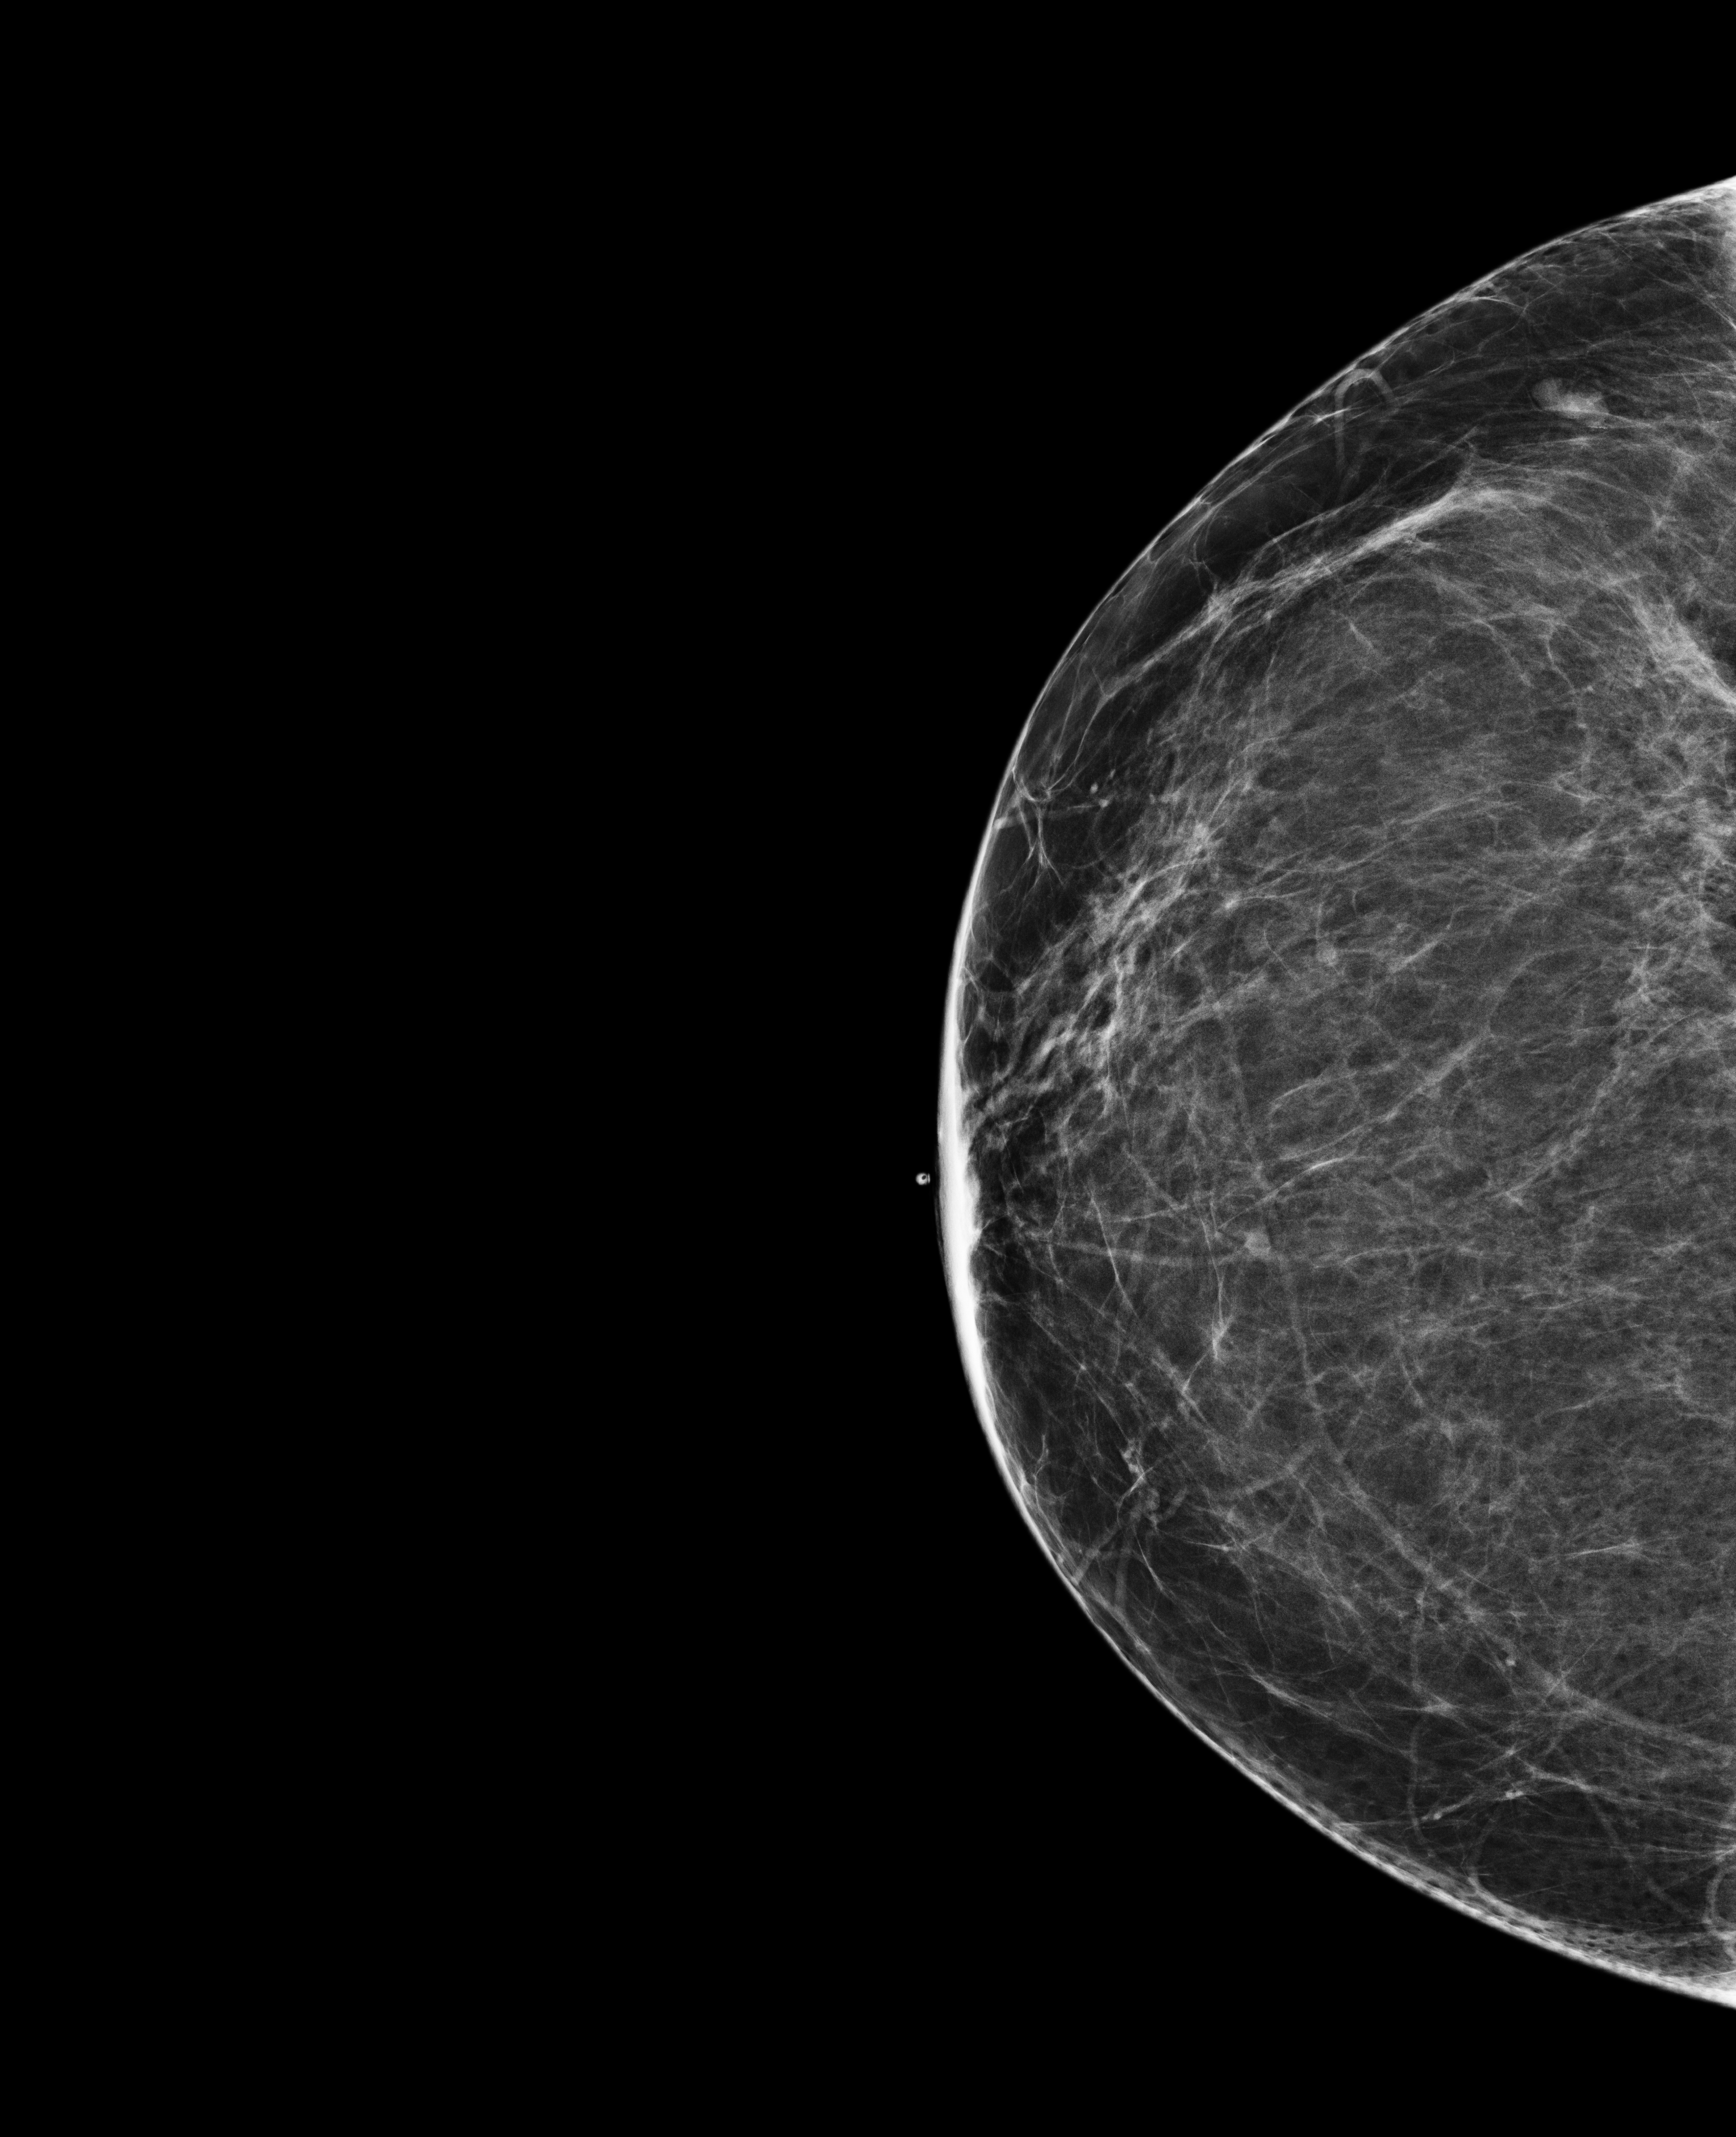
Annual screening mammography examination. Patient aged 52 years (female).
Image type: full-field digital mammogram. Breast: right. Projection: CC view, nipple in profile.